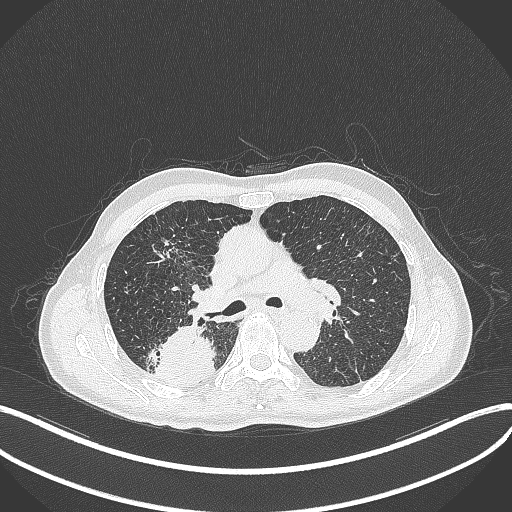
Chest CT, one axial slice. Position 287 of 428 along the scan axis. 120 kVp. Lung window (W 1500 / L -600 HU). 512 × 512 image matrix, field of view 400 × 400 mm. Patient: male, 79 years. Case-level facts recorded for this patient, not image findings: clinical TNM (as recorded): T3 N0 M0.
Annotated regions visible in this slice (bounding box drawn by a radiologist):
- lung tumour (recorded histology: adenocarcinoma): bounding box <156,321,216,388> (left, top, right, bottom; pixels)